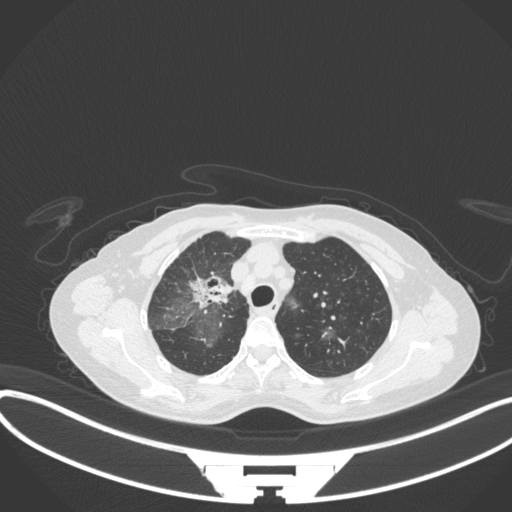
Chest CT, one axial slice; position 245 of 311 along the scan axis; 120 kVp; lung window (W 1500 / L -600 HU); 1 mm slice thickness; 512 × 512 image matrix. Patient: female, 59 years. From the clinical record (not read from this slice): clinical TNM (as recorded): T3 N0 M0.
Annotated regions visible in this slice (rectangle marked by the reading radiologist):
- lung tumour (recorded histology: adenocarcinoma): bounding box [x1, y1, x2, y2] px = [185, 266, 238, 317]